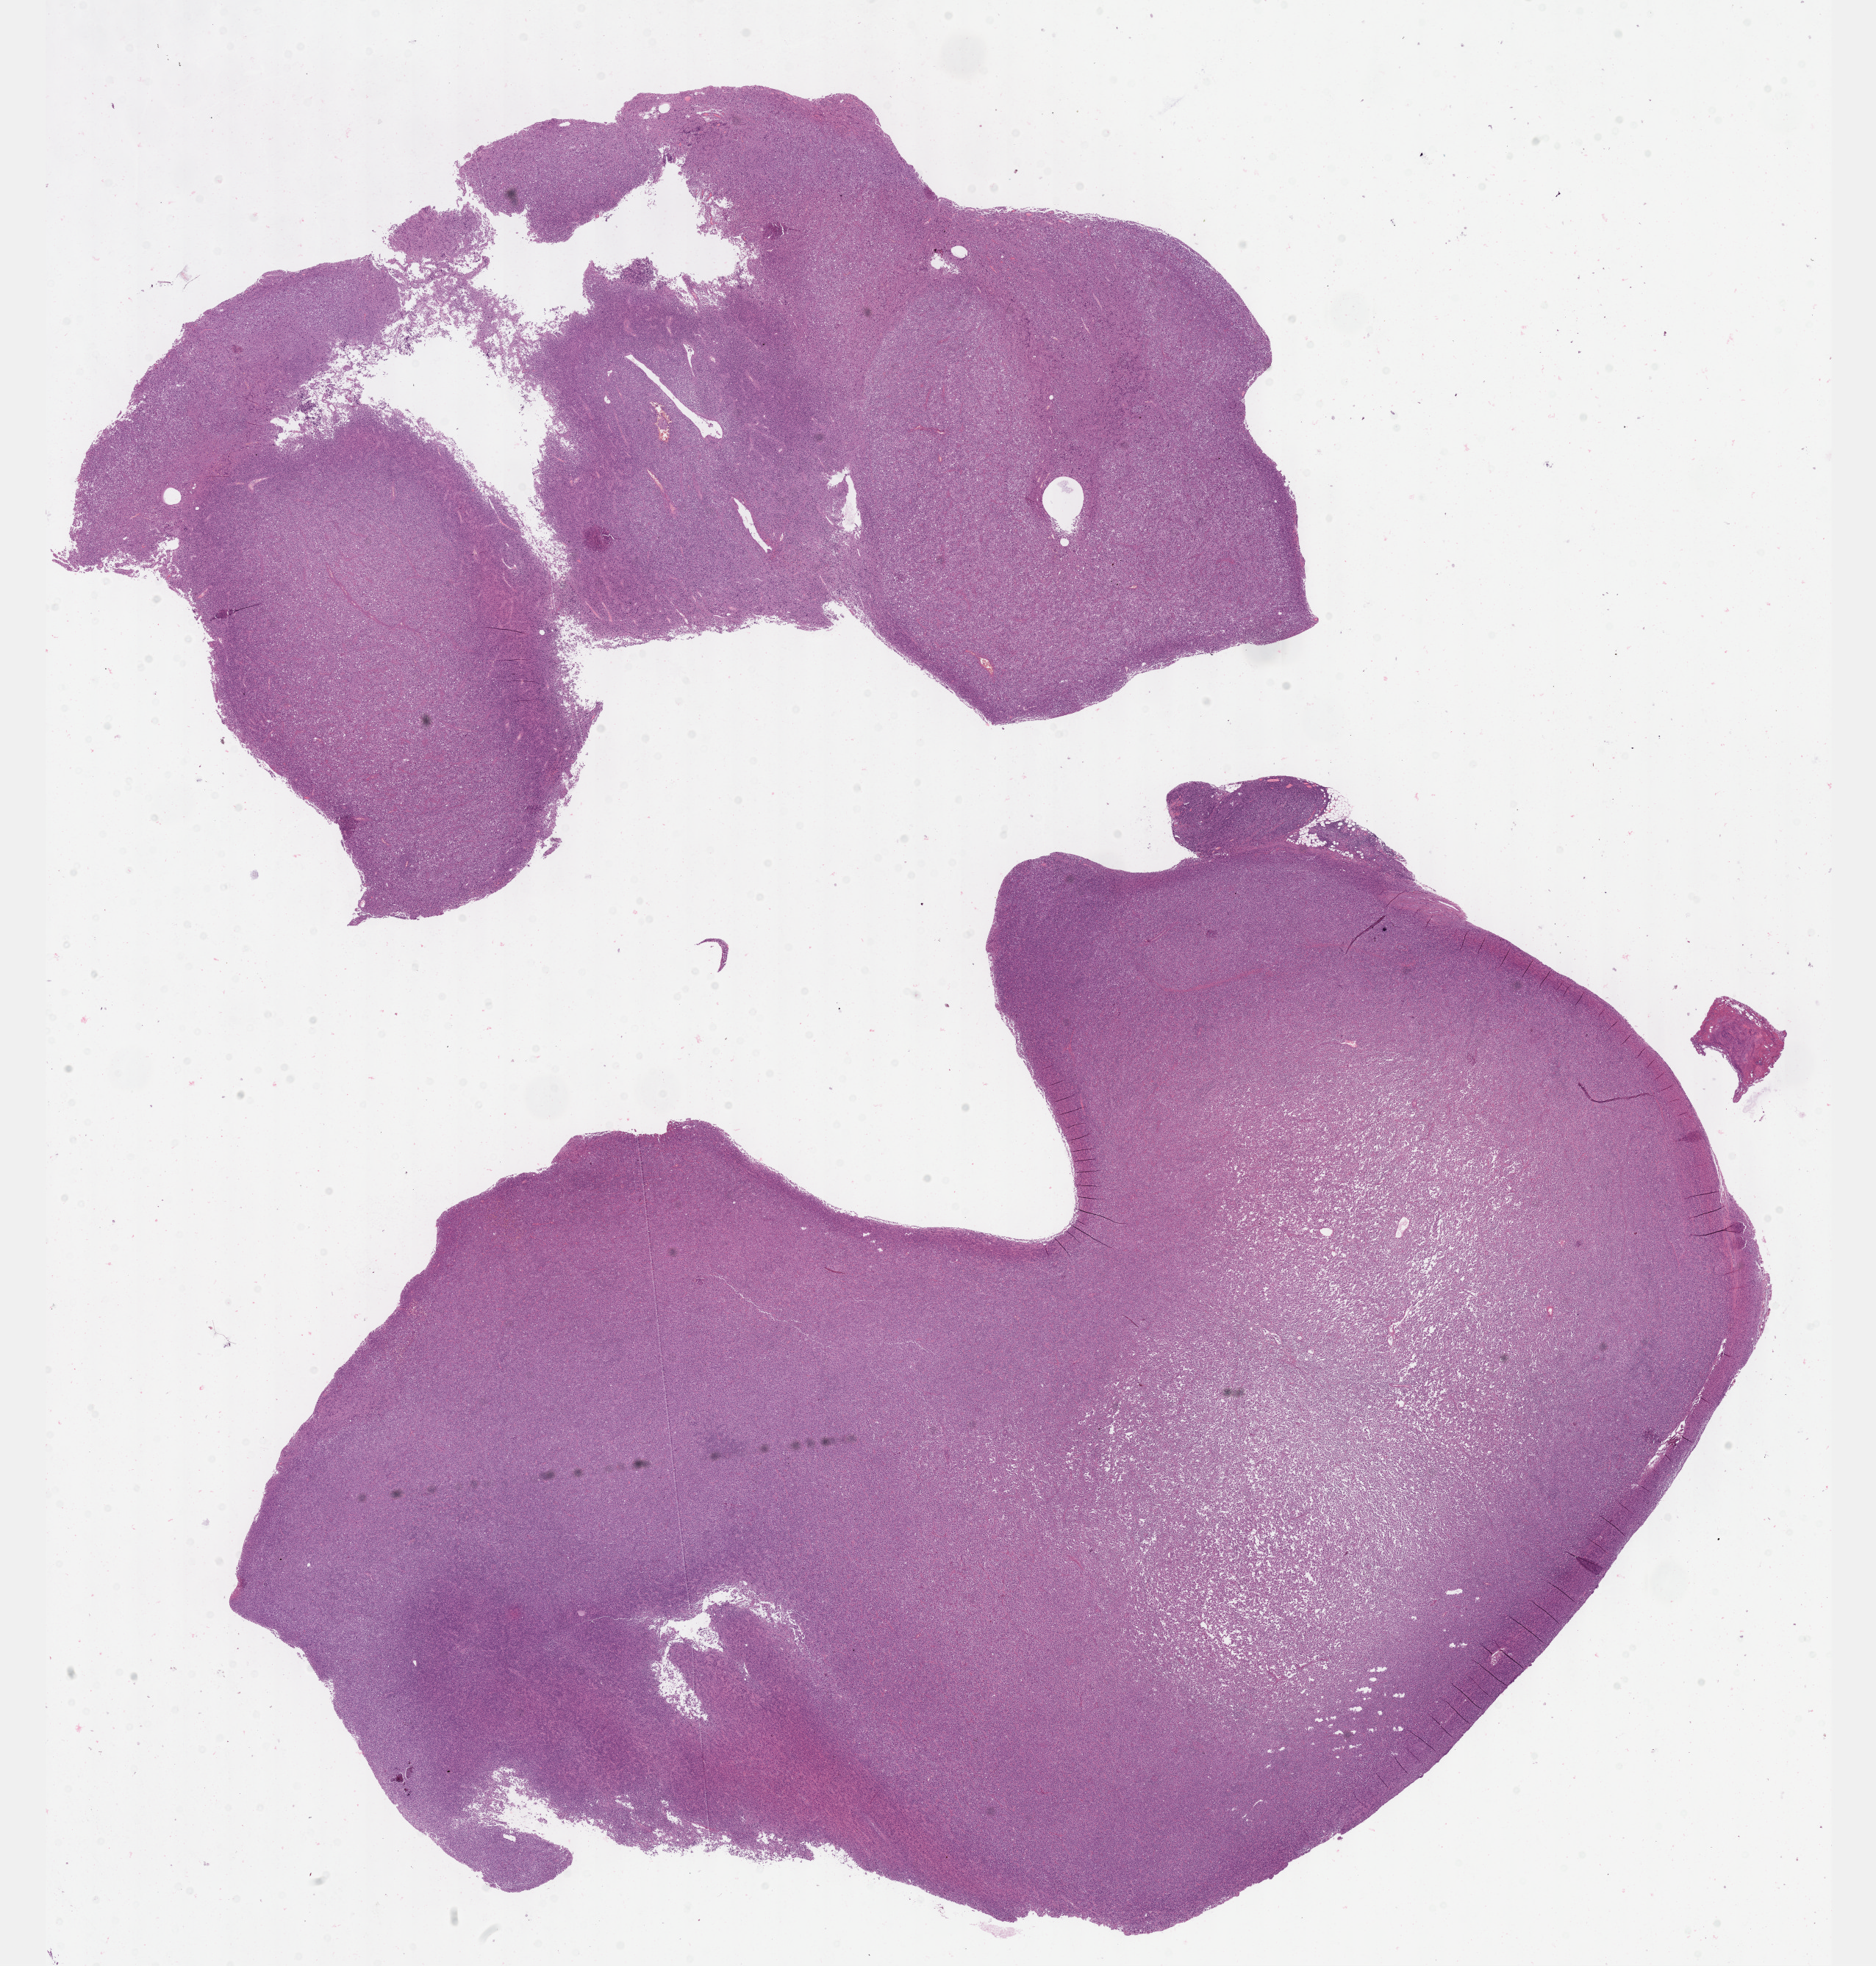
Whole-slide histology image, Hematoxylin and eosin (H&E) stained, shown as a low-resolution overview of the whole scanned area (about 20.6 x 21.6 mm); formalin-fixed paraffin-embedded (FFPE) diagnostic section; lymphoid tissue, primary tumour sample. Patient: male, age at initial diagnosis 51 years.
* diagnosis: Mediastinal (thymic) large B-cell lymphoma (lymph nodes of head, face and neck)